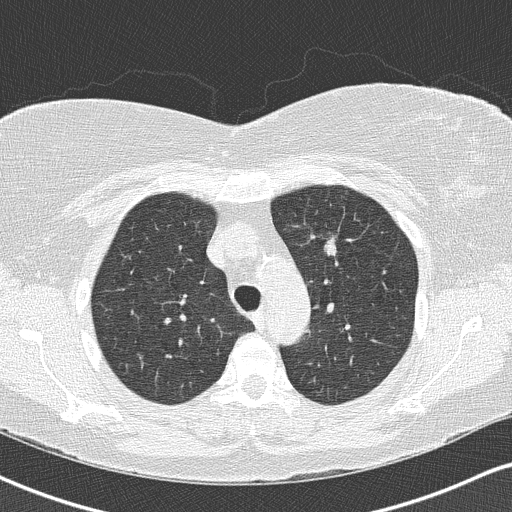
Low-dose screening chest CT, one axial slice; 120 kVp; lung window (W 1500 / L -600 HU); 512 × 512 image matrix, field of view 328 × 328 mm.
Structures marked on this image (manually delineated by an expert):
- lesion 1 (tumor, upper lobe of left lung): bounding box (x1, y1, x2, y2) in pixels: (323, 235, 338, 257)